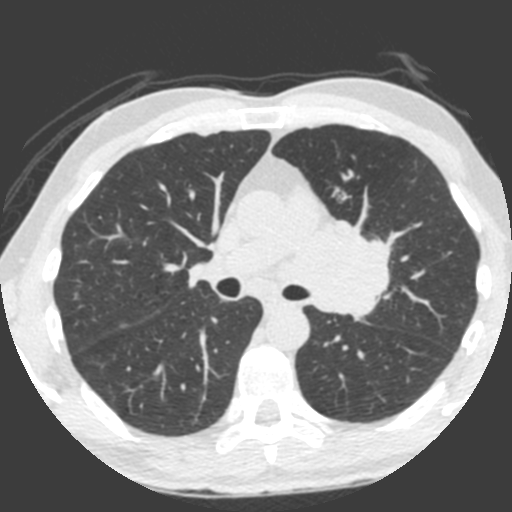
Axial slice from a low-dose chest CT screening exam. Third screening round (two years after baseline). Lung window (W 1500 / L -600 HU). Standard (soft-tissue) reconstruction kernel (B). 120 kVp. Slice 134 of 212 in the series. Male, age 55 years at enrolment. Current smoker at enrolment.
• Expert reader's lesion annotation, box from (x=309, y=217) to (x=398, y=325) px.
• Reader record for this screening exam (exam-level; its link to the box is not recorded): non-calcified nodule or mass ≥4 mm, left upper lobe, 49 × 29 mm, spiculated (stellate) margins, soft tissue attenuation, pre-existing on the prior screen: yes; interval growth: yes.